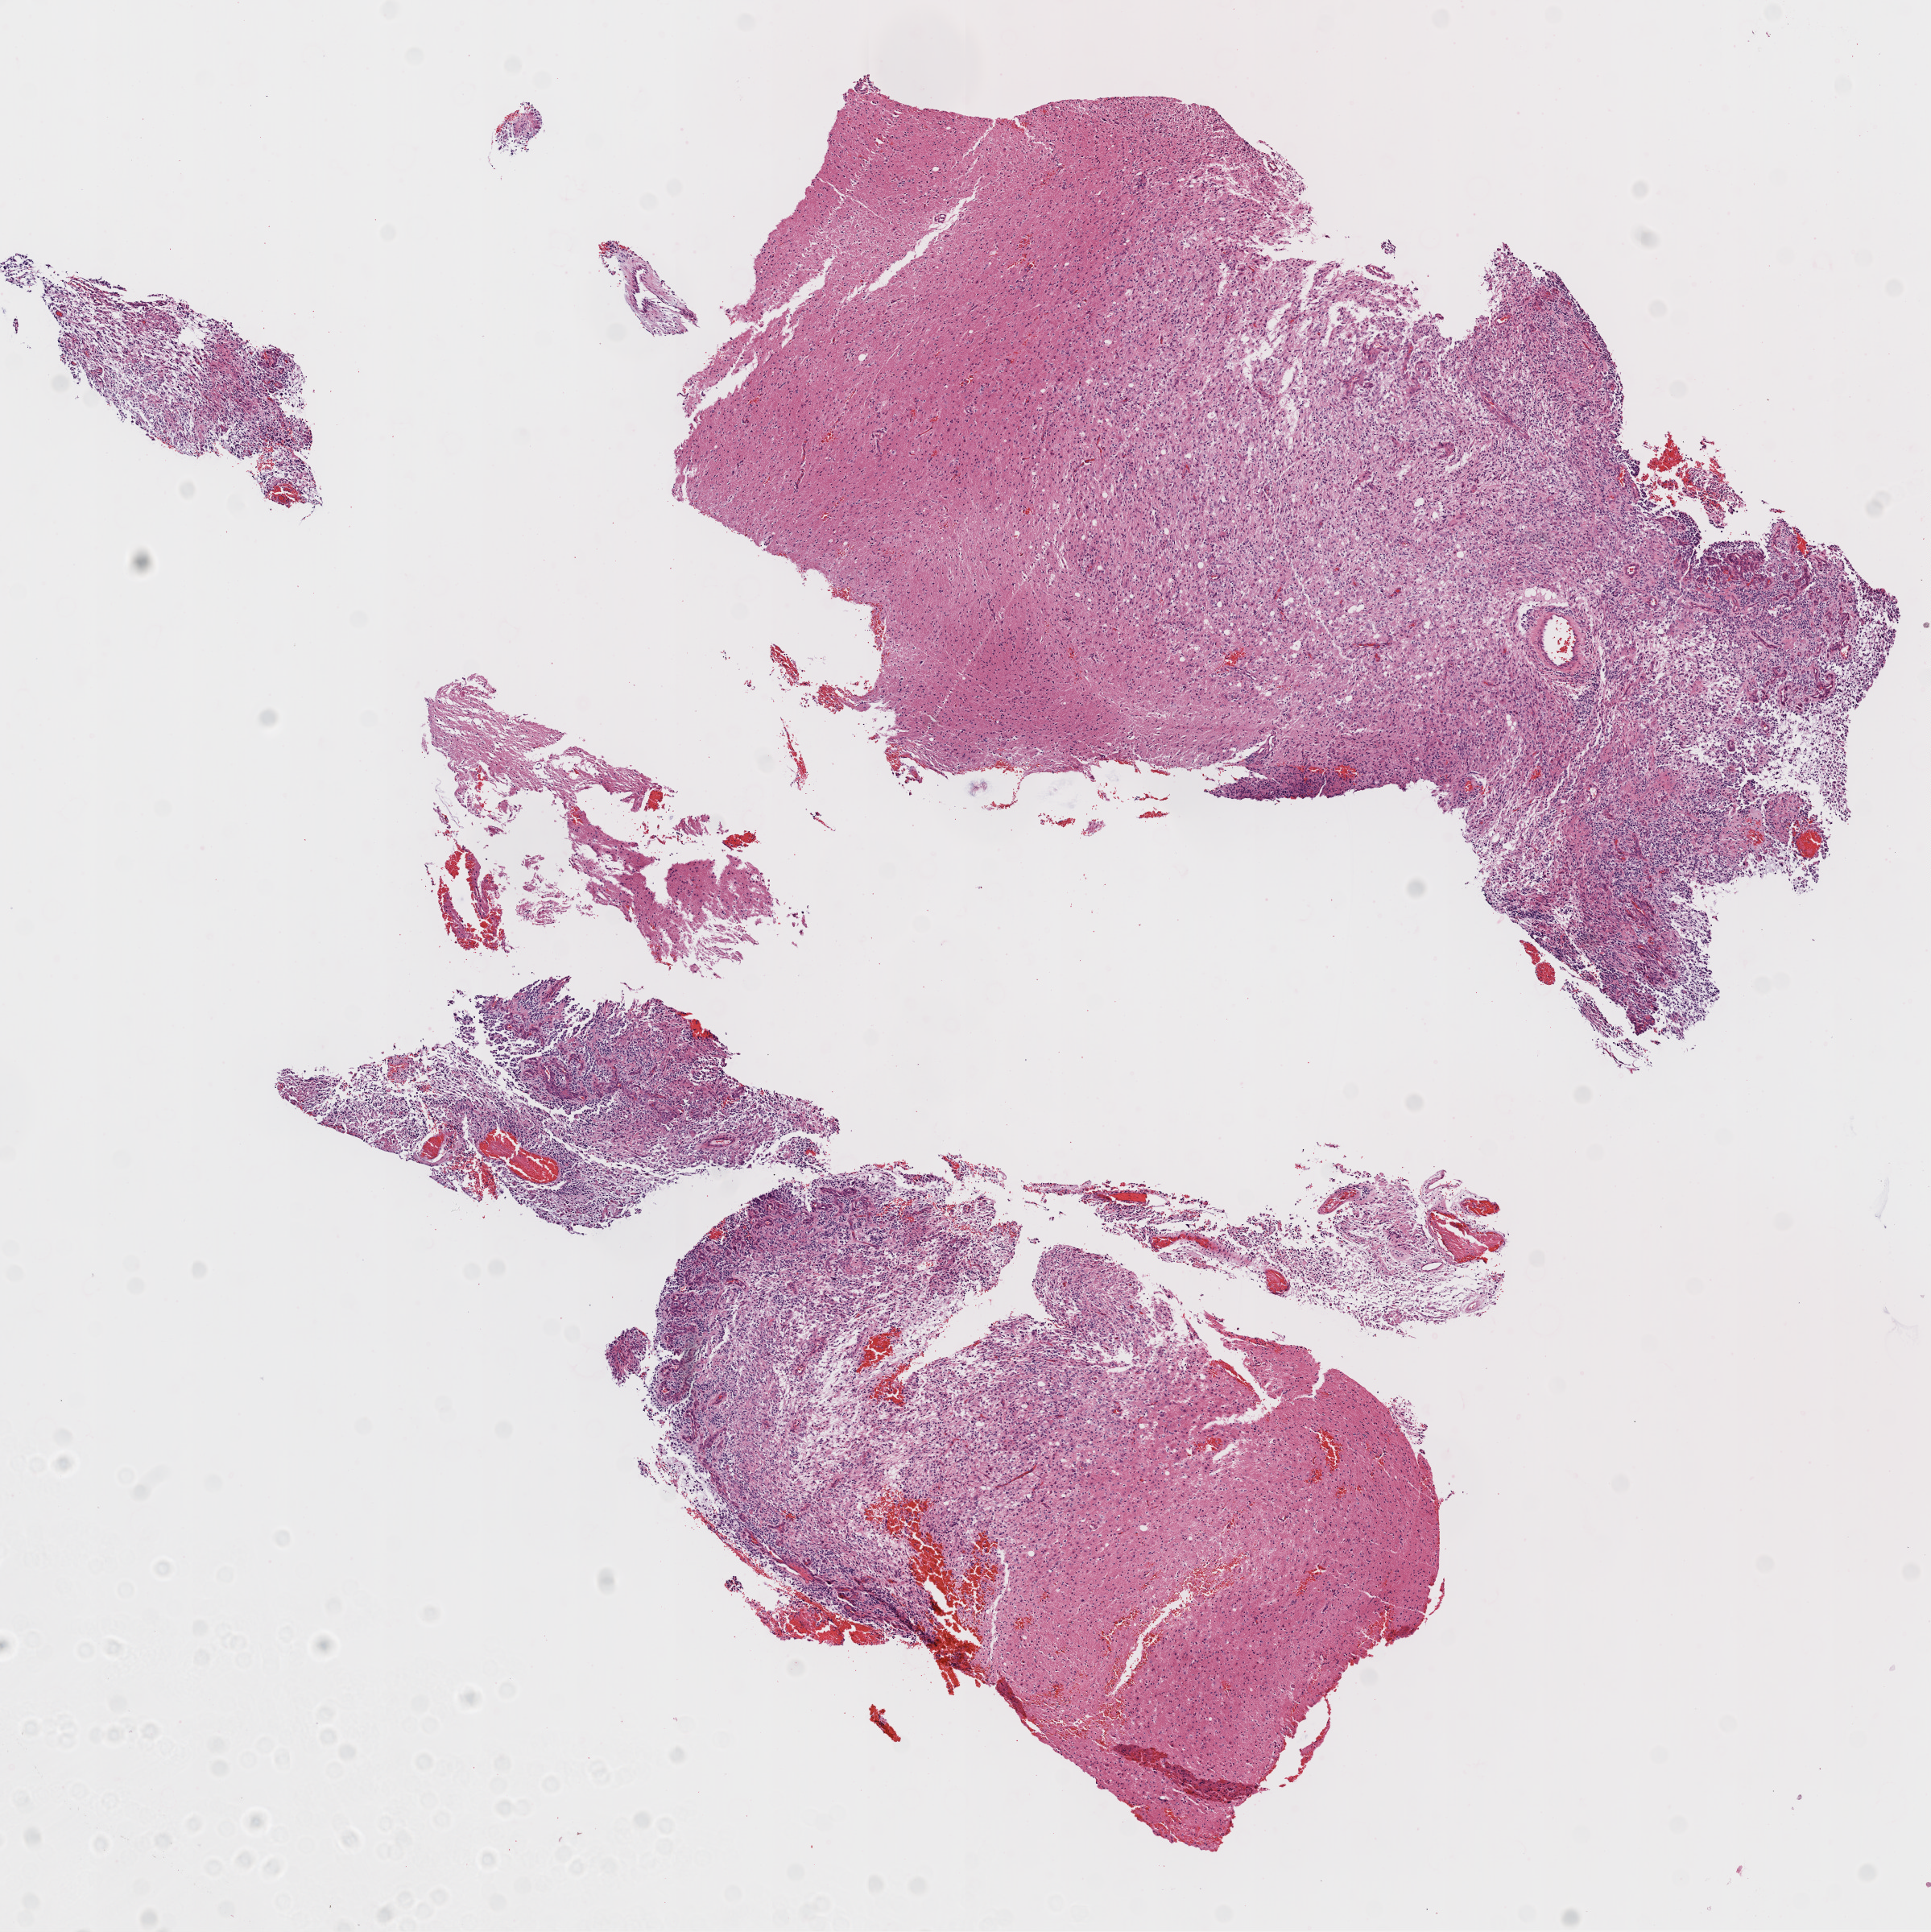
Whole-slide histology image, Hematoxylin and eosin (H&E) stained — whole scanned area (about 9.7 x 9.7 mm, acquisition: 20x scan) shown as a low-resolution overview; formalin-fixed paraffin-embedded (FFPE) diagnostic section; brain, primary tumour sample. Male patient; age at initial diagnosis 51 years.
* histologic diagnosis: Glioblastoma